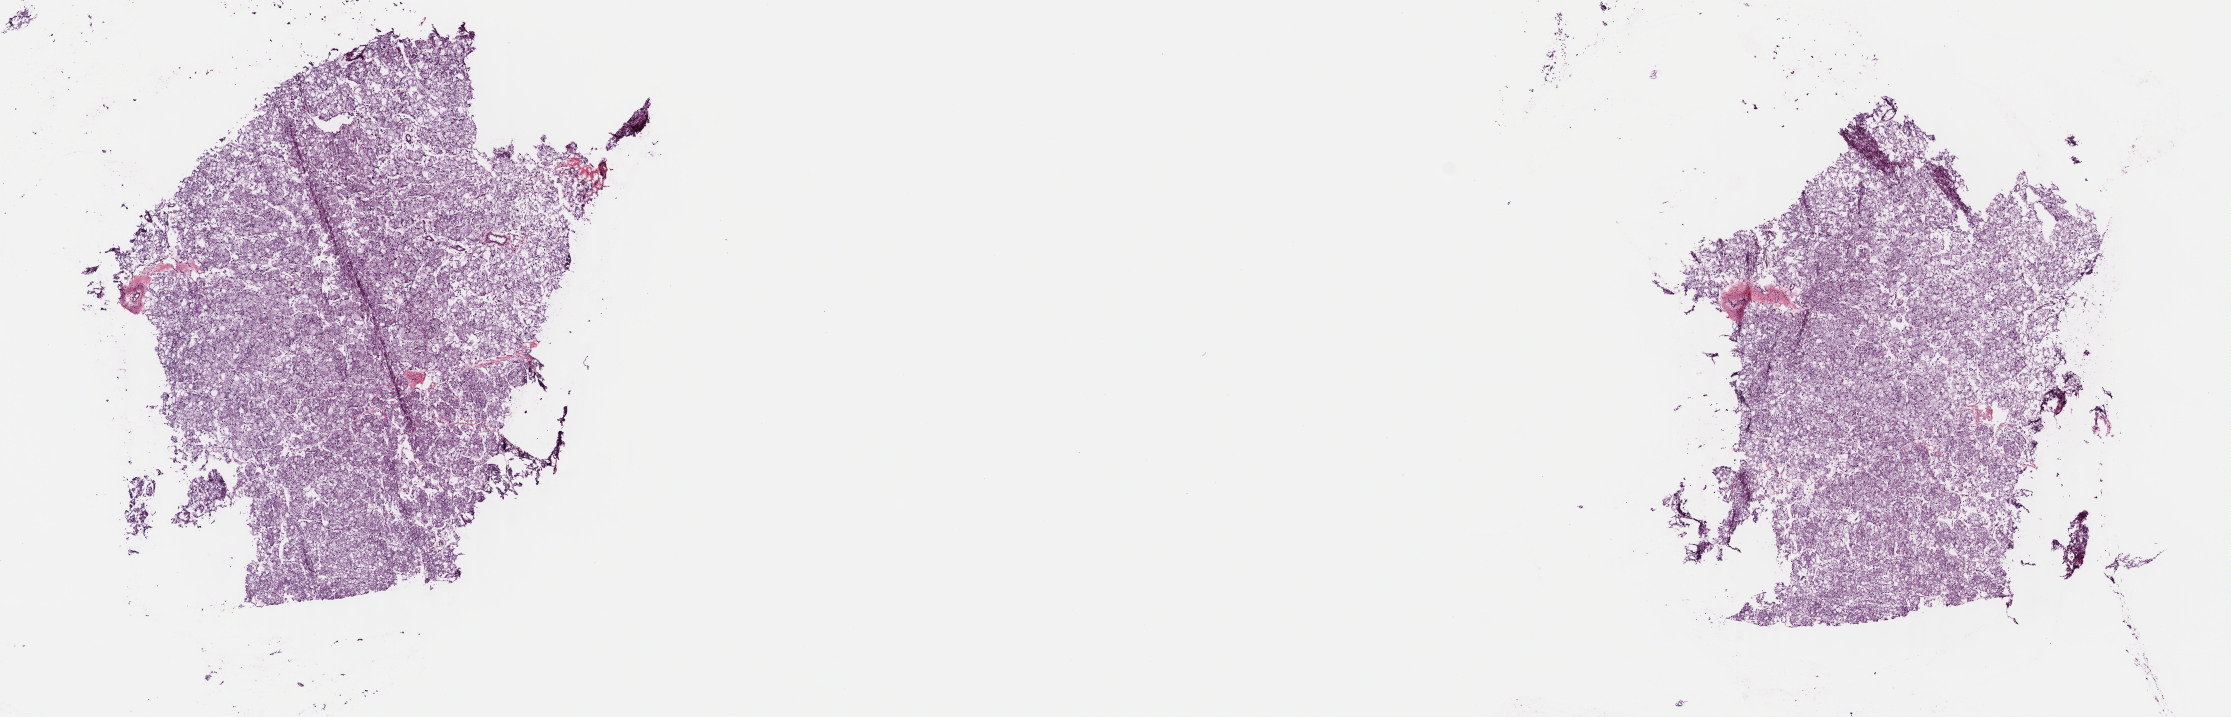
Digitized Hematoxylin and eosin (H&E) stained tissue section (whole slide), low-resolution overview of the scanned area, about 17.5 x 5.6 mm; frozen section; sample: primary tumour, kidney. Female patient; age at initial diagnosis 43 years. Pathologist review of this section (percent, as recorded): tumour cells 100%, tumour nuclei 80%, normal cells 0%, stromal cells 0%, necrosis 0%. Inflammatory infiltration, as recorded: lymphocyte infiltration 2%, monocyte infiltration 2%, neutrophil infiltration 0%.
- AJCC pathologic stage: I (7th edition)
- diagnosis: Renal cell carcinoma, chromophobe type